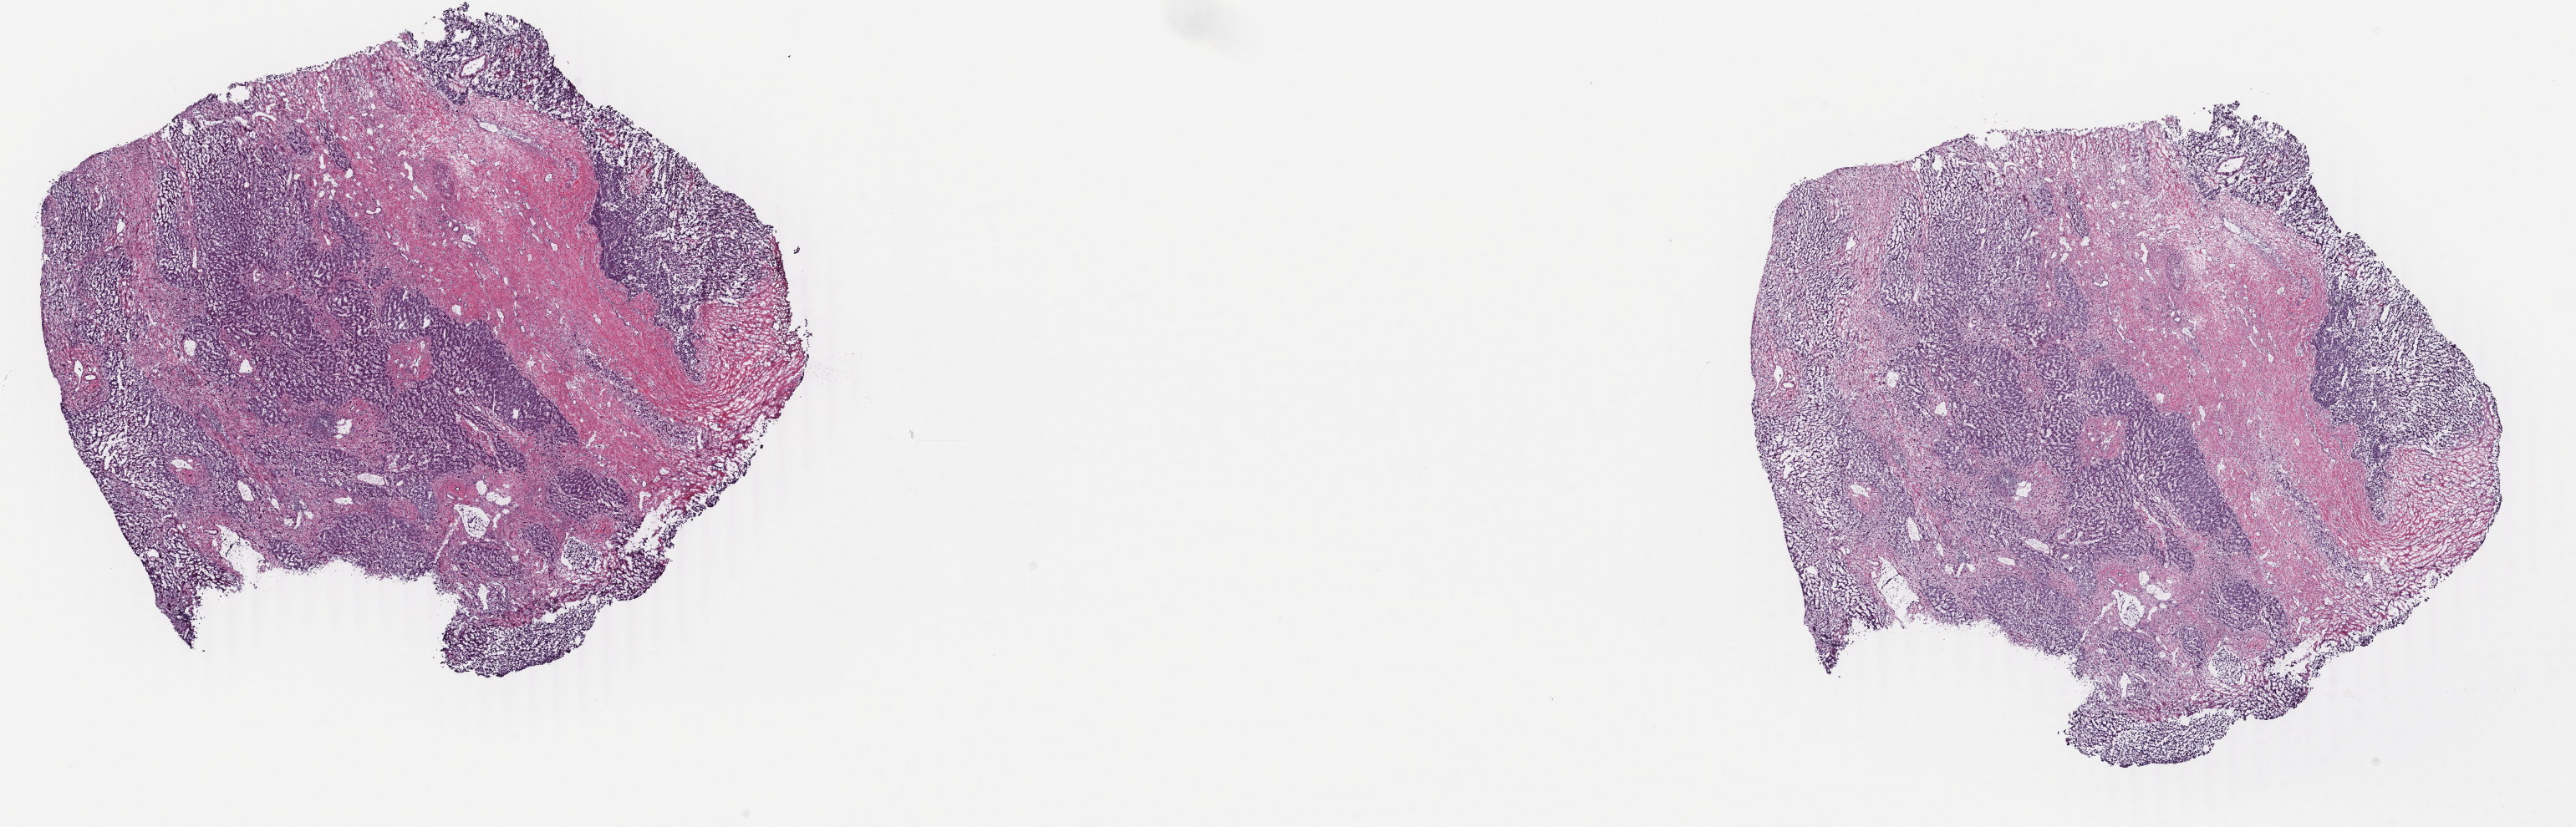
Digitized Hematoxylin and eosin (H&E) stained tissue section (whole slide), whole scanned area (about 24.5 x 7.9 mm, acquisition: 40x scan) shown as a low-resolution overview. Frozen section from the top of the tissue portion. Liver, primary tumour sample. Female, age 51 years at initial diagnosis. Histologic grade: G1 (well differentiated). Pathologist review of this section (percent, as recorded): tumour cells 60%, tumour nuclei 60%, normal cells 0%, stromal cells 40%, necrosis 0%. Inflammatory infiltration, as recorded: lymphocyte infiltration 5%, monocyte infiltration 0%, neutrophil infiltration 0%.
Histologic diagnosis: Hepatocellular carcinoma, NOS.